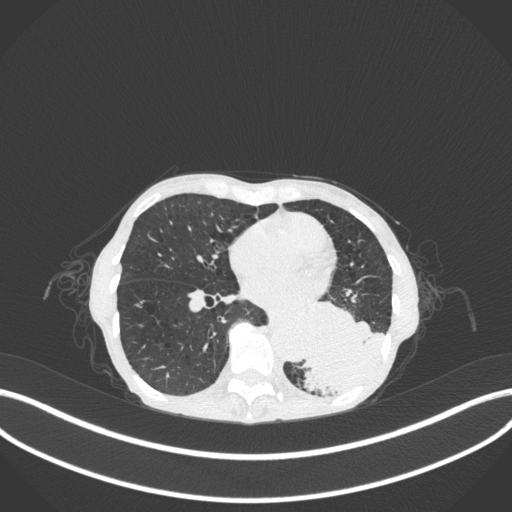
Chest CT, one axial slice. Slice 110 of 347 in the series (ordered by position). 120 kVp. Lung window (W 1500 / L -600 HU). 512 × 512 image matrix, field of view 400 × 400 mm. Patient: female, 70 years. From the clinical record (not read from this slice): clinical TNM (as recorded): T3 N0 M0; histopathological grade: G3.
Outlined on this slice (bounding box drawn by a radiologist):
- lung tumour (recorded histology: small cell carcinoma): bounding box (x1, y1, x2, y2) in pixels: (299, 290, 390, 396)